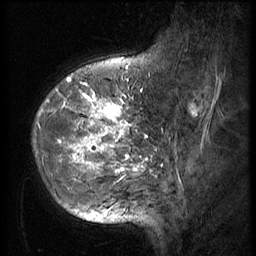
Breast MRI (dynamic contrast-enhanced), one sagittal slice. Position 15 of 56 along the scan axis. 3 images stored at this slice position (order not interpretable as contrast timing). 1.5 T. TE 4.2 ms, TR 9 ms. 2.5 mm slice thickness. 256 × 256 image matrix, field of view 180 × 180 mm. Female patient, age 49 years. From the clinical record (not read from this slice): setting: breast cancer imaged before/during neoadjuvant chemotherapy; receptor status: HER2-positive.
Annotated regions visible in this slice (semi-automatic segmentation, software-assisted and operator-edited):
- analysis volume of interest (the breast-tissue region the enhancement analysis was run in; not a lesion): bounding box [x1, y1, x2, y2] px = [32, 79, 144, 203]
- tumour enhancement mask (voxels above the 140 % enhancement threshold inside the analysis volume of interest): [39, 79, 143, 178]